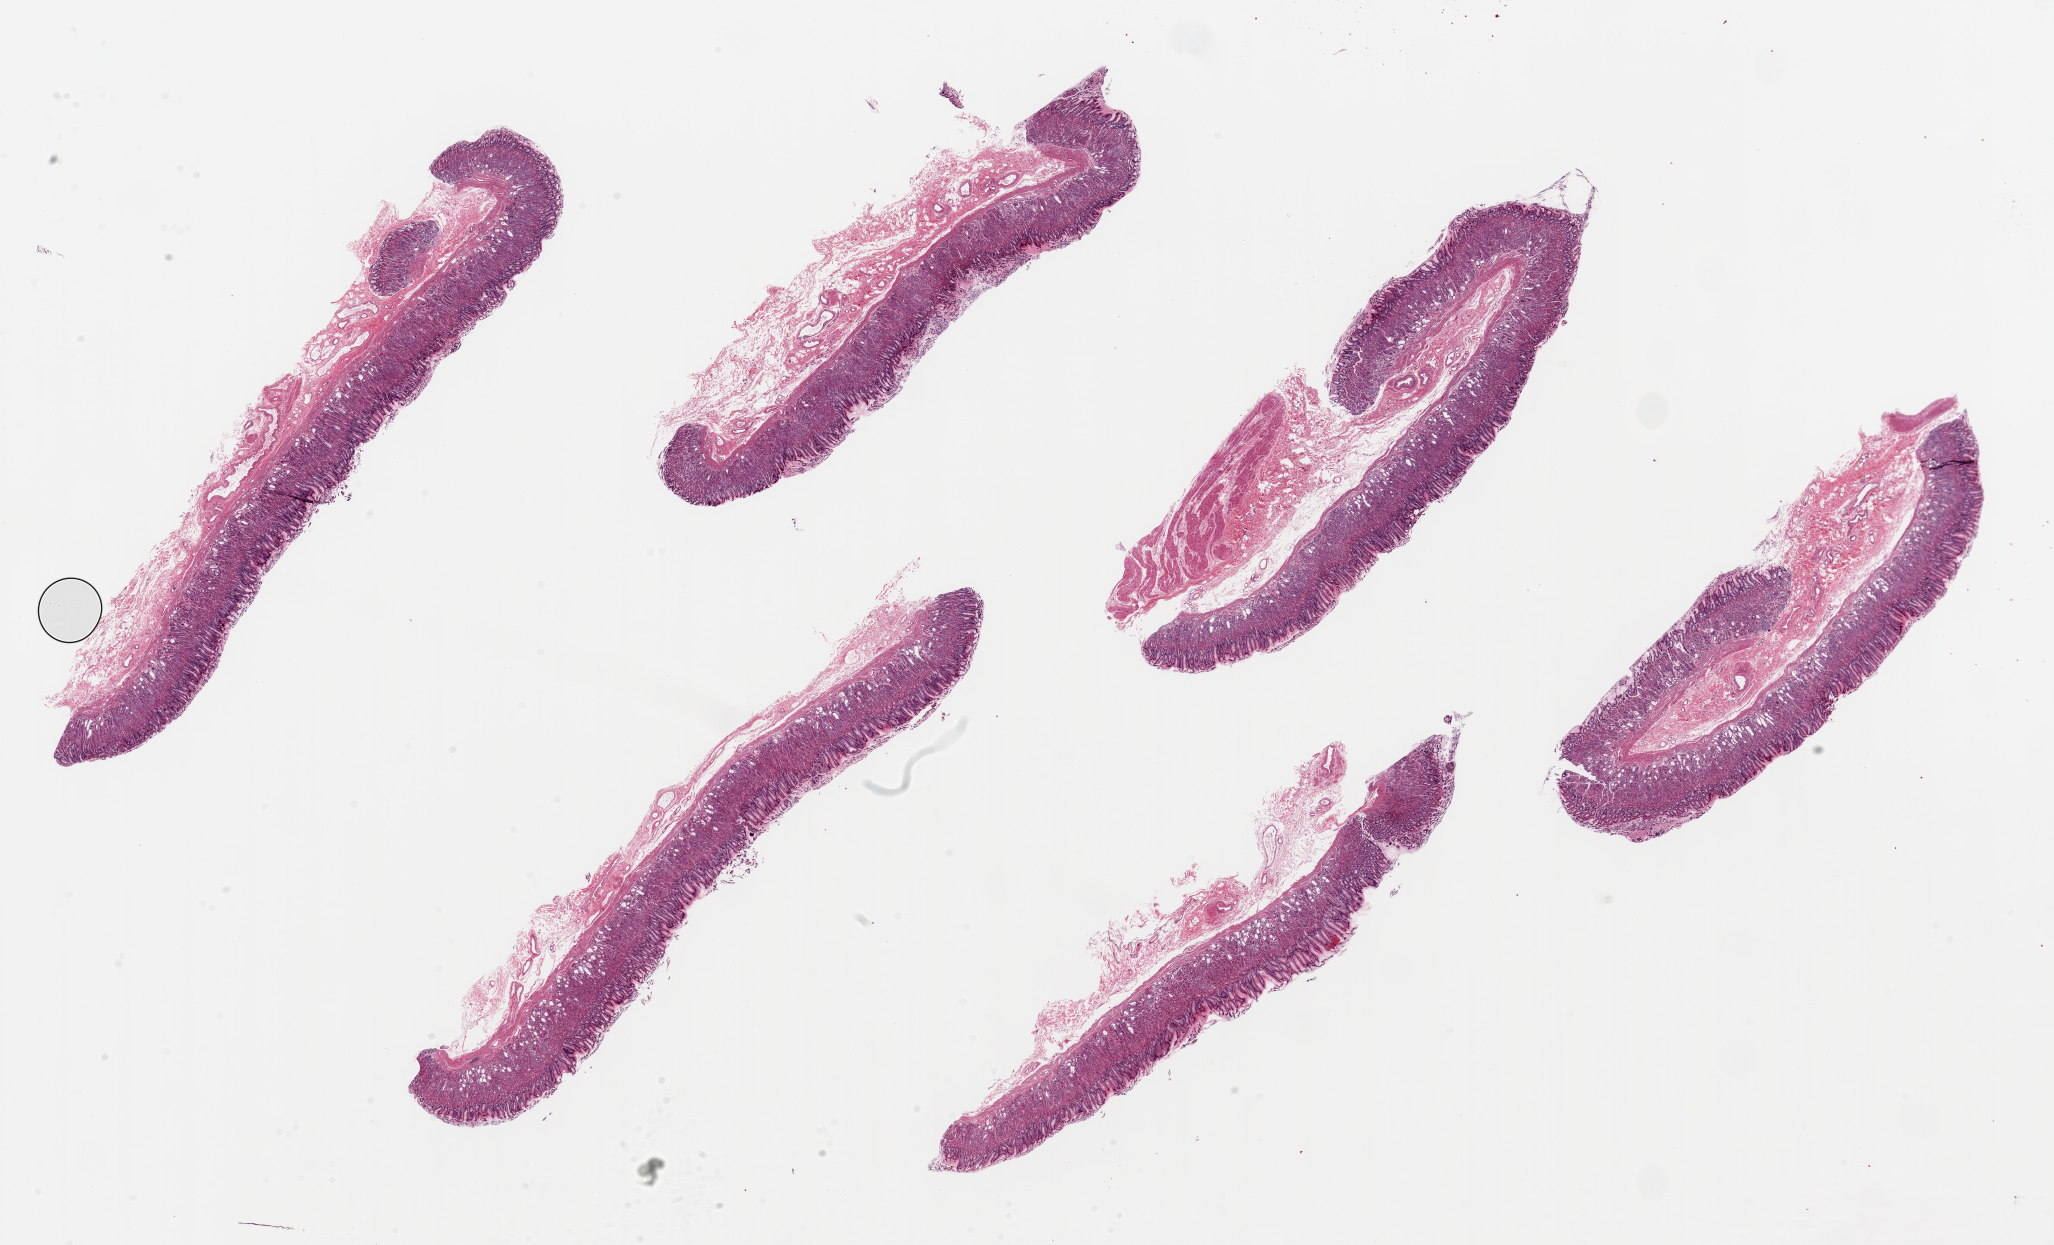
Whole-slide image, H&E stain, low-resolution overview of the scanned area, about 32.5 x 19.7 mm, PAXgene-fixed paraffin-embedded (PFPE) section, section of stomach (target tissue), donor tissue sample. Male donor.
Pathologist's review note for this sample: 6 pieces, up to 12x2.5mm; ~50-70% thickness is well preserved mucosa.